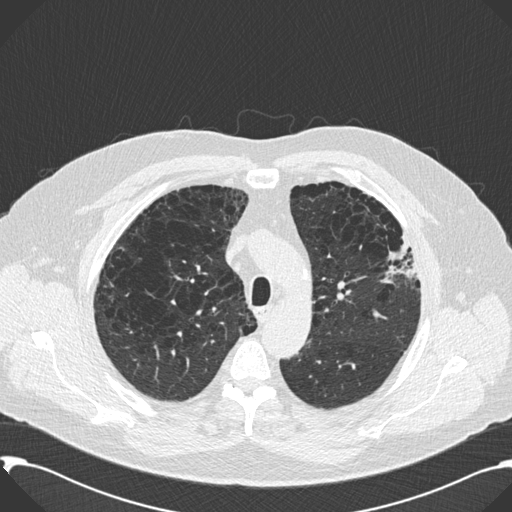
Chest CT (low-dose screening protocol), one axial image. Second annual screen. Lung window (W 1500 / L -600 HU). 2 mm slice thickness. 512 × 512 image matrix. Male participant, aged 59 years at enrolment. Current smoker at enrolment.
• Expert-annotated lung lesion, bounding box (x1, y1, x2, y2) in pixels: (363, 213, 420, 297).
• Screening reader's record for this exam: no non-calcified nodule ≥4 mm recorded.
• Official screen result: negative screen, significant abnormalities not suspicious for lung cancer.